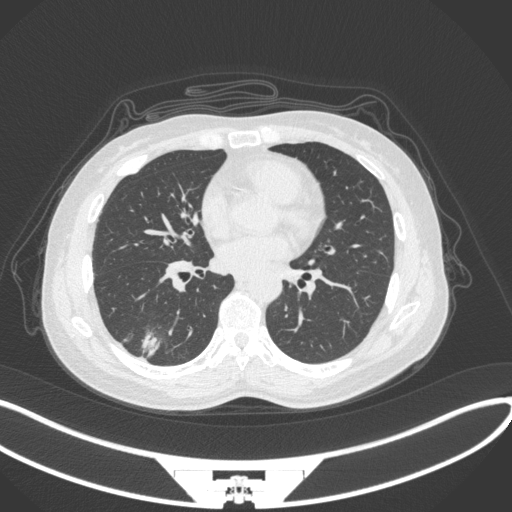
Chest CT, one axial slice; slice 134 of 352 in the series (ordered by position); 120 kVp; lung window (W 1500 / L -600 HU); 1 mm slice thickness; 512 × 512 image matrix. Patient: female, 55 years. Case-level facts recorded for this patient, not image findings: clinical TNM (as recorded): T1c N1 M0.
Annotated regions visible in this slice (rectangle marked by the reading radiologist):
- lung tumour (recorded histology: adenocarcinoma): bounding box (x1, y1, x2, y2) in pixels: (138, 322, 168, 360)